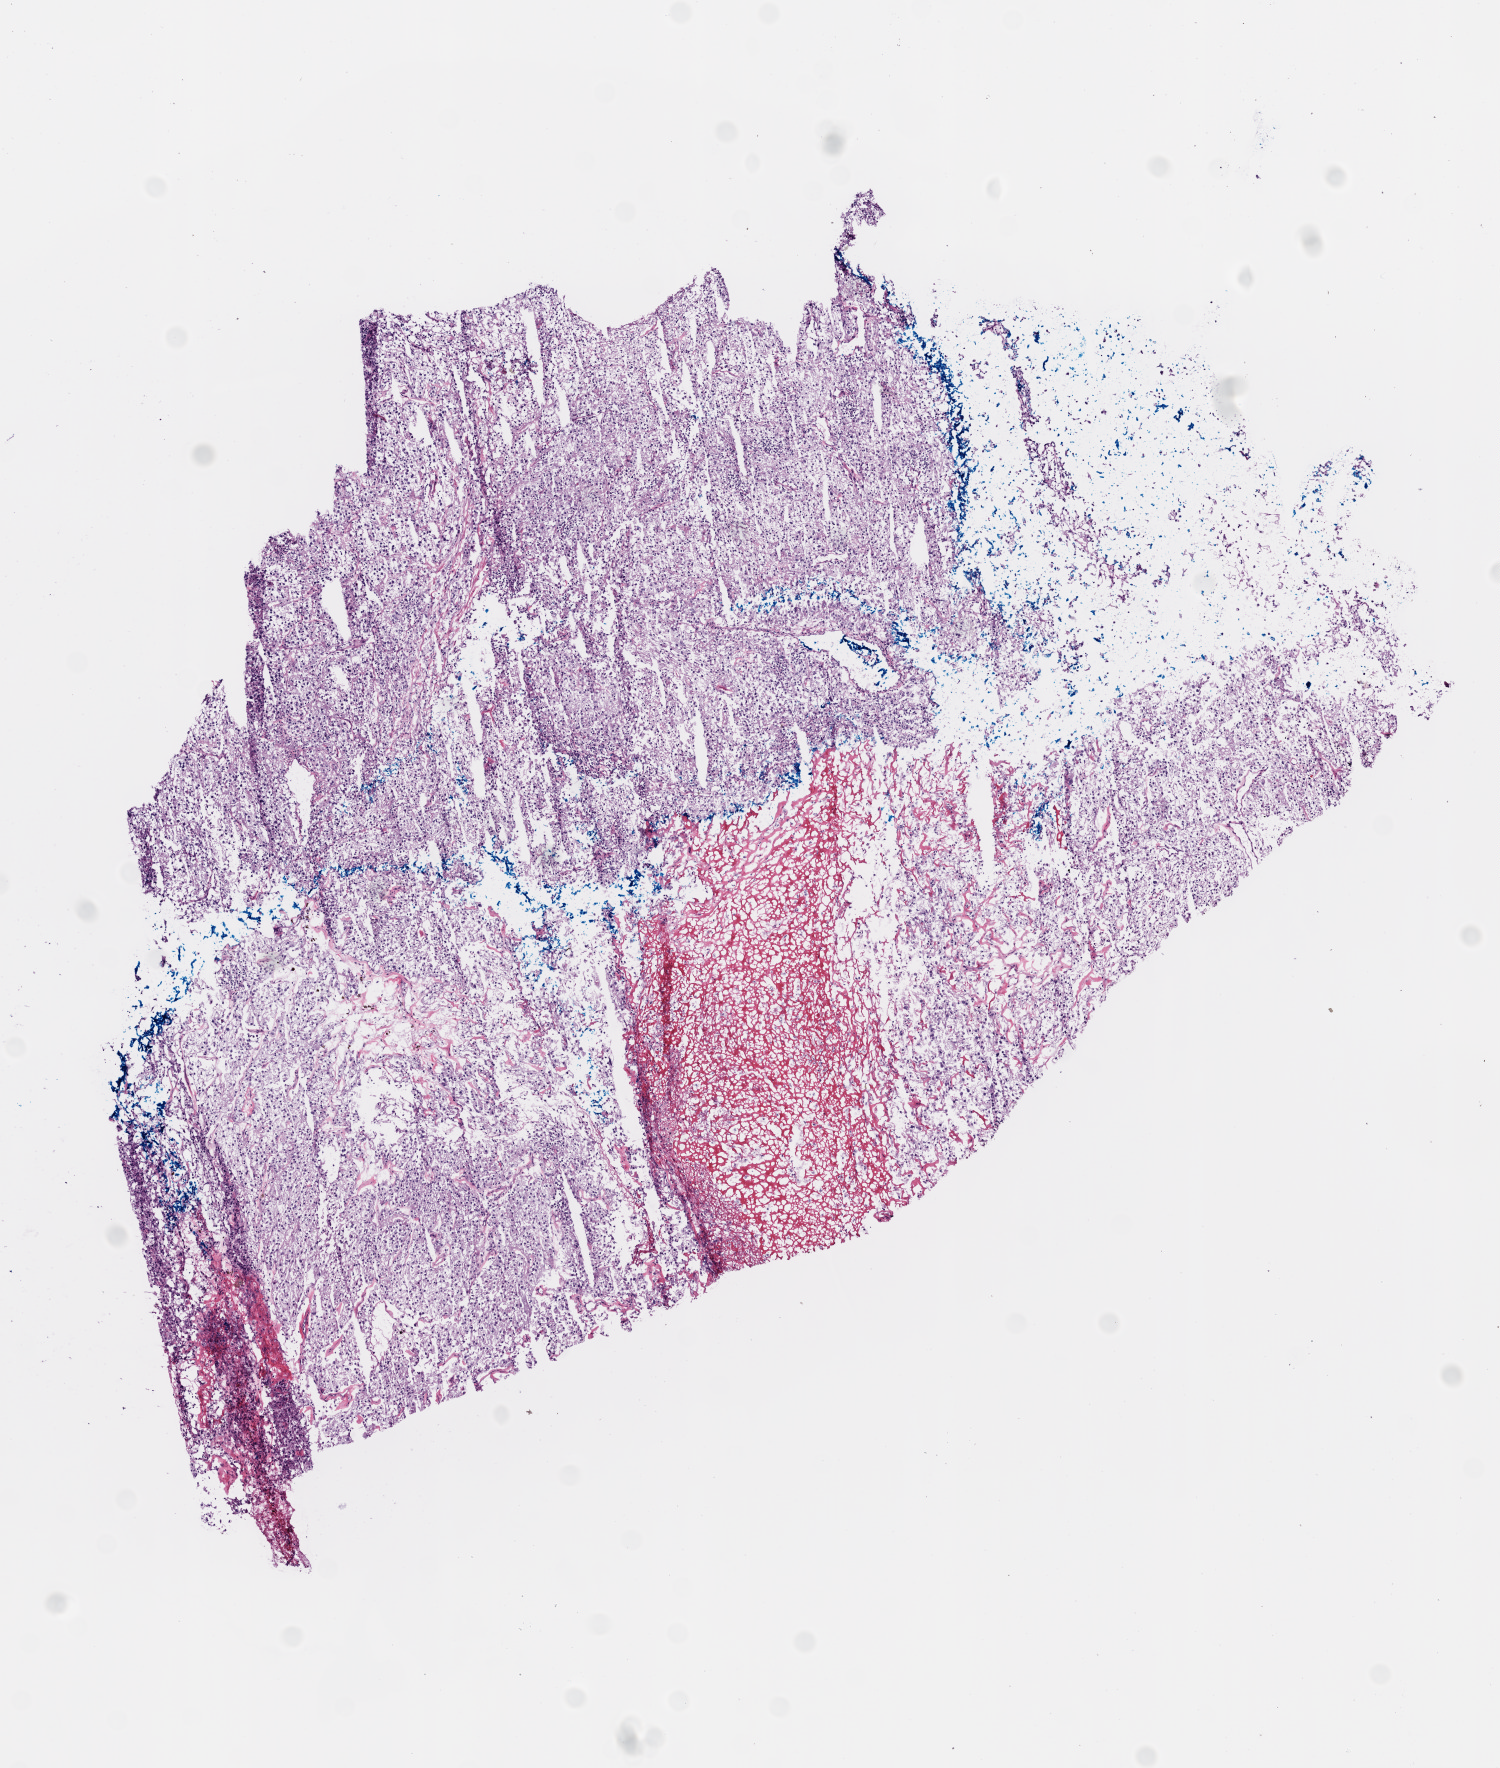
Whole-slide histology image, H&E, shown as a low-resolution overview of the whole scanned area (about 6.0 x 7.1 mm, from a 20x scan); frozen section from the top of the tissue portion; kidney, primary tumour sample. Female patient; age at initial diagnosis 75 years. Histologic grade: G4 (undifferentiated). Pathologist review of this section (percent, as recorded): tumour cells 80%, tumour nuclei 80%, normal cells 0%, stromal cells 5%, necrosis 15%.
• laterality: right
• AJCC pathologic stage: I
• histologic diagnosis: Clear cell adenocarcinoma, NOS
• TNM: T1 NX M0